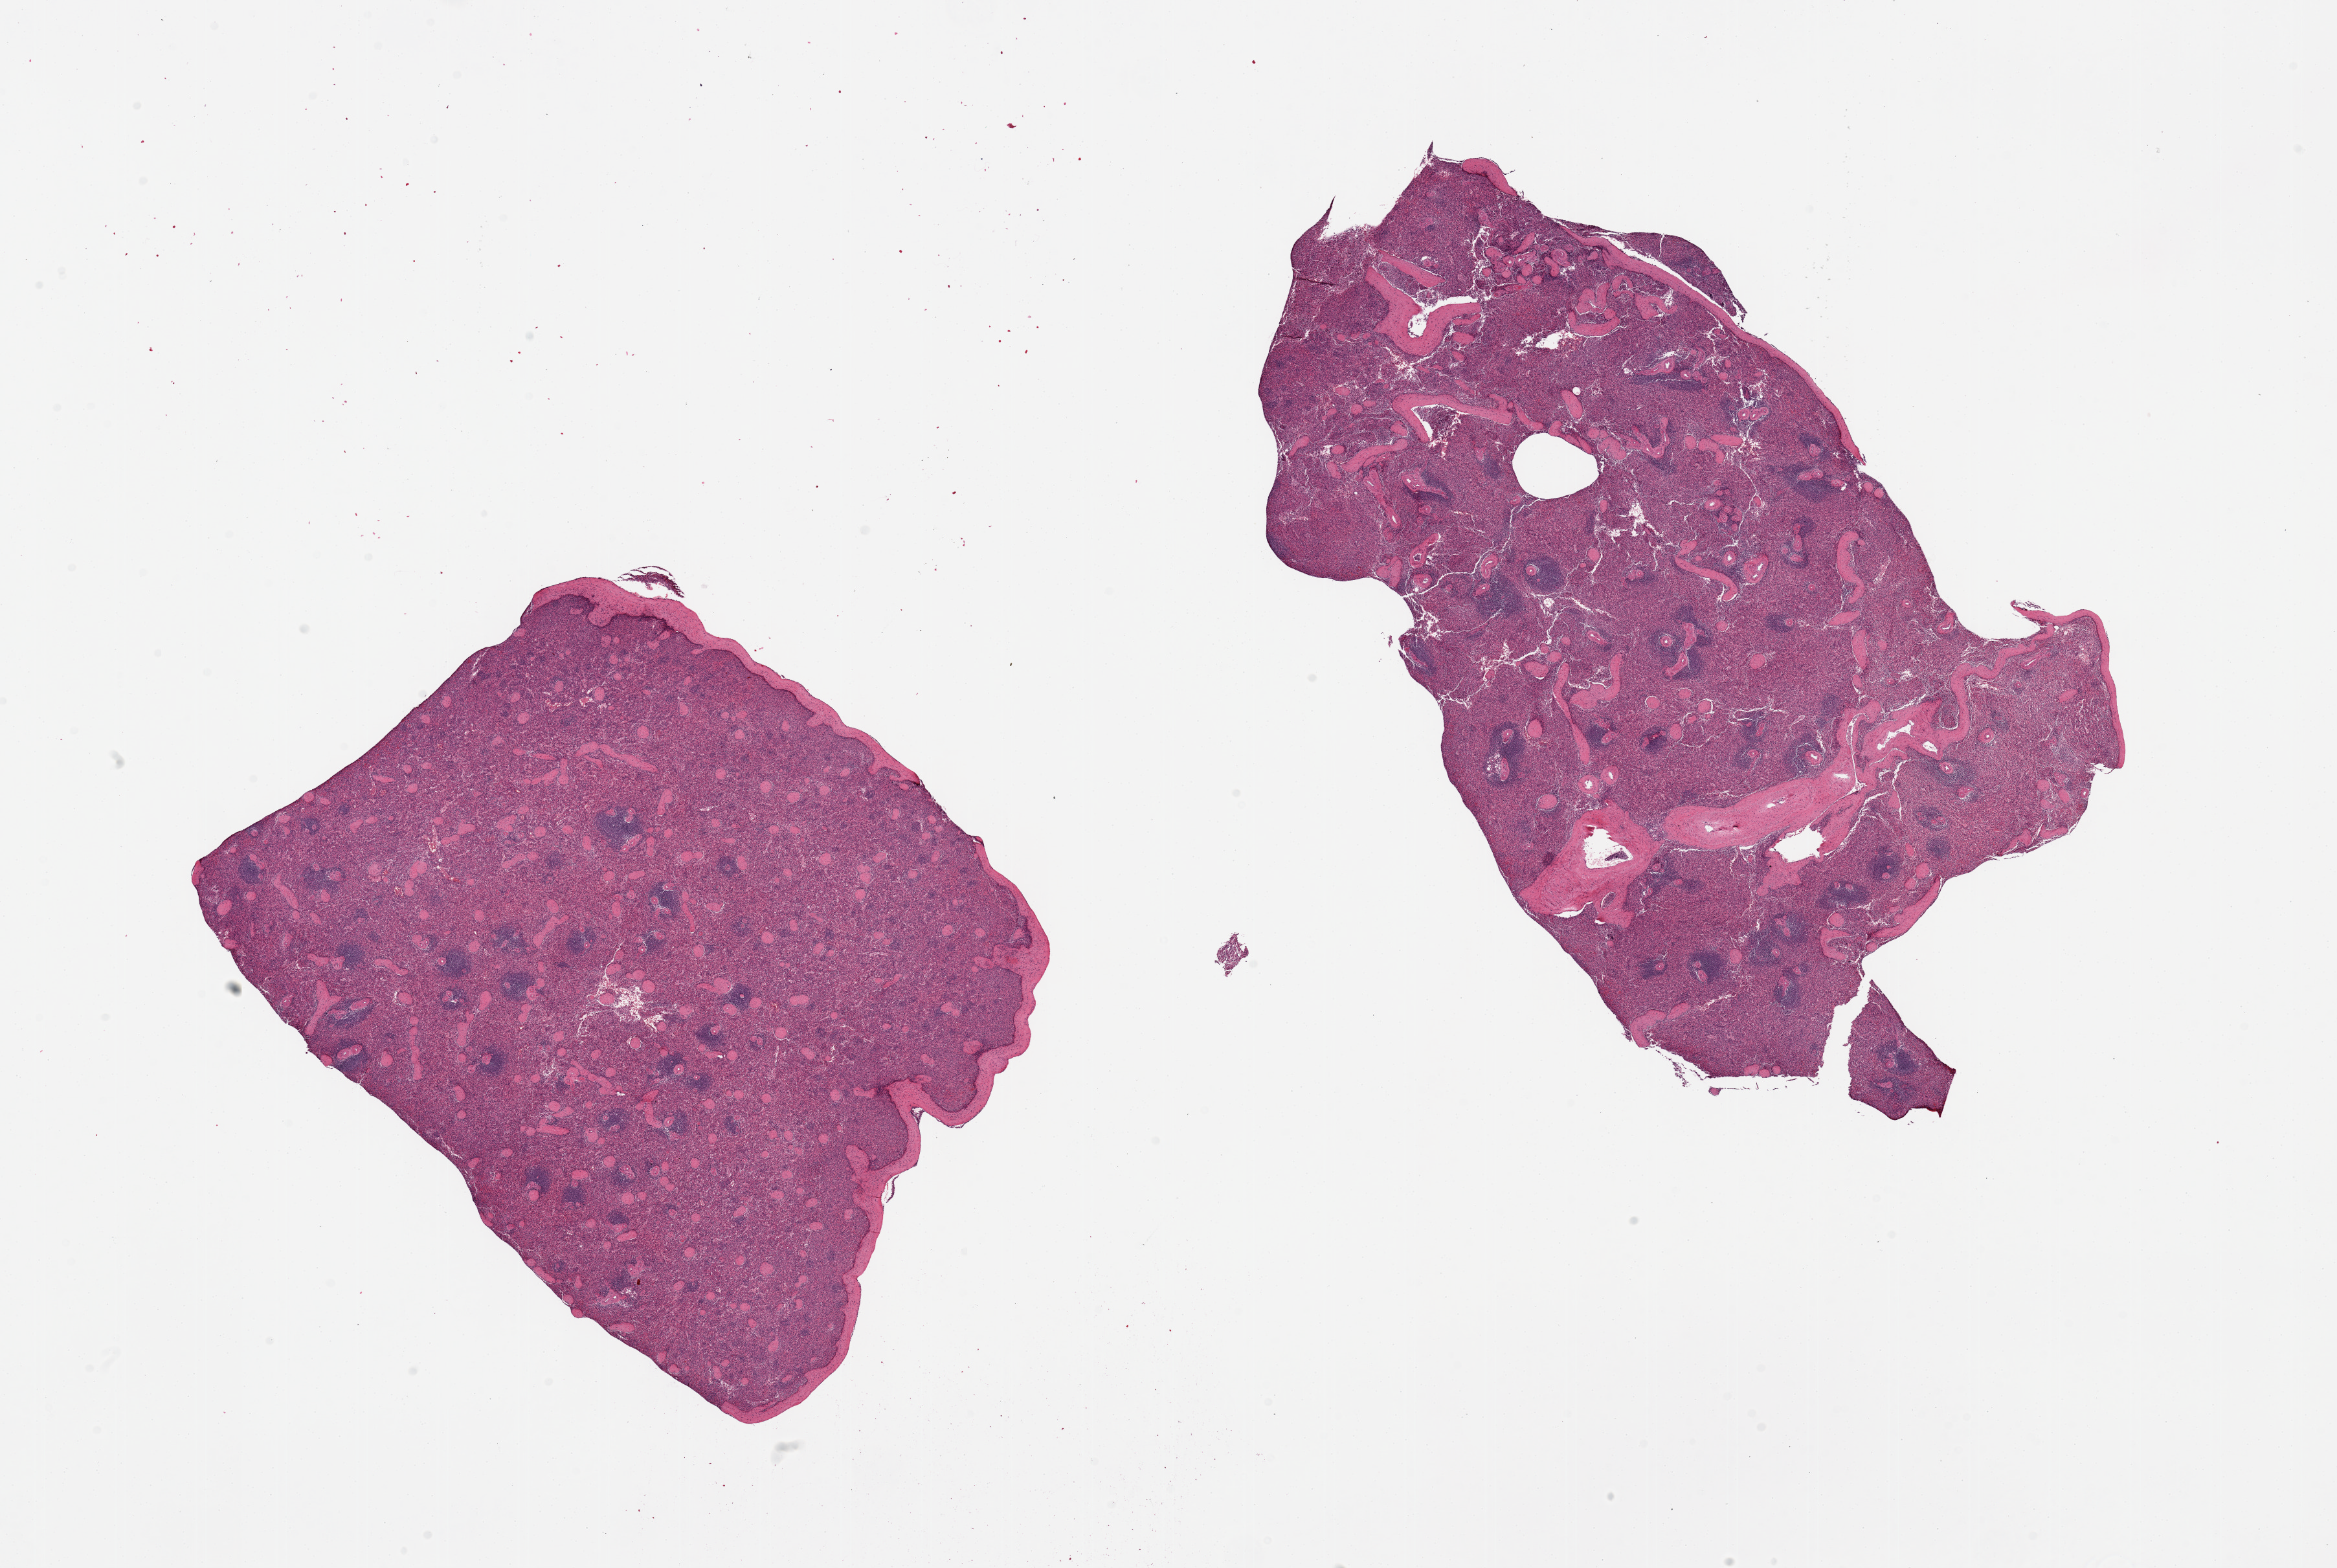
H&E whole-slide image, brightfield, whole scanned area (about 28.5 x 19.2 mm, slide scanned at 20x) shown as a low-resolution overview, PAXgene-fixed paraffin-embedded (PFPE) section, section of spleen (target tissue), tissue donor sample. Donor: male.
Review note (as recorded): 2 pieces, 11x6 & 9x6mm moderate congestion.